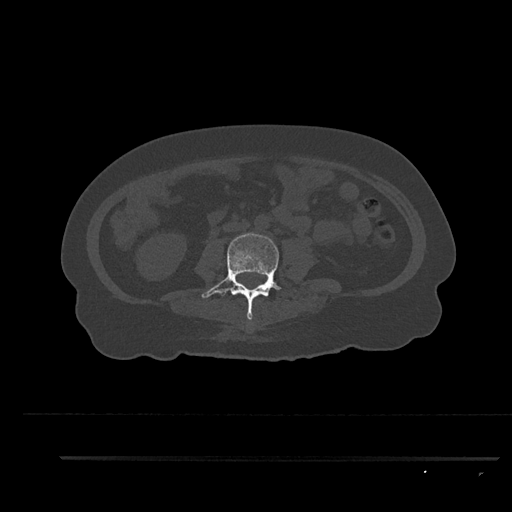
CT including the spine, one axial slice; position 85 of 797 along the scan axis; reconstruction kernel Br40s/3; 120 kVp; bone window (W 1800 / L 400 HU); 0.5 mm slice thickness; 512 × 512 image matrix. Patient: female, 44 years. Case-level facts recorded for this patient, not image findings: primary cancer: renal.
Structures marked on this image (semi-automatic segmentation, software-assisted and operator-edited):
- L3 vertebra: bounding box [x1, y1, x2, y2] px = [202, 233, 287, 320]